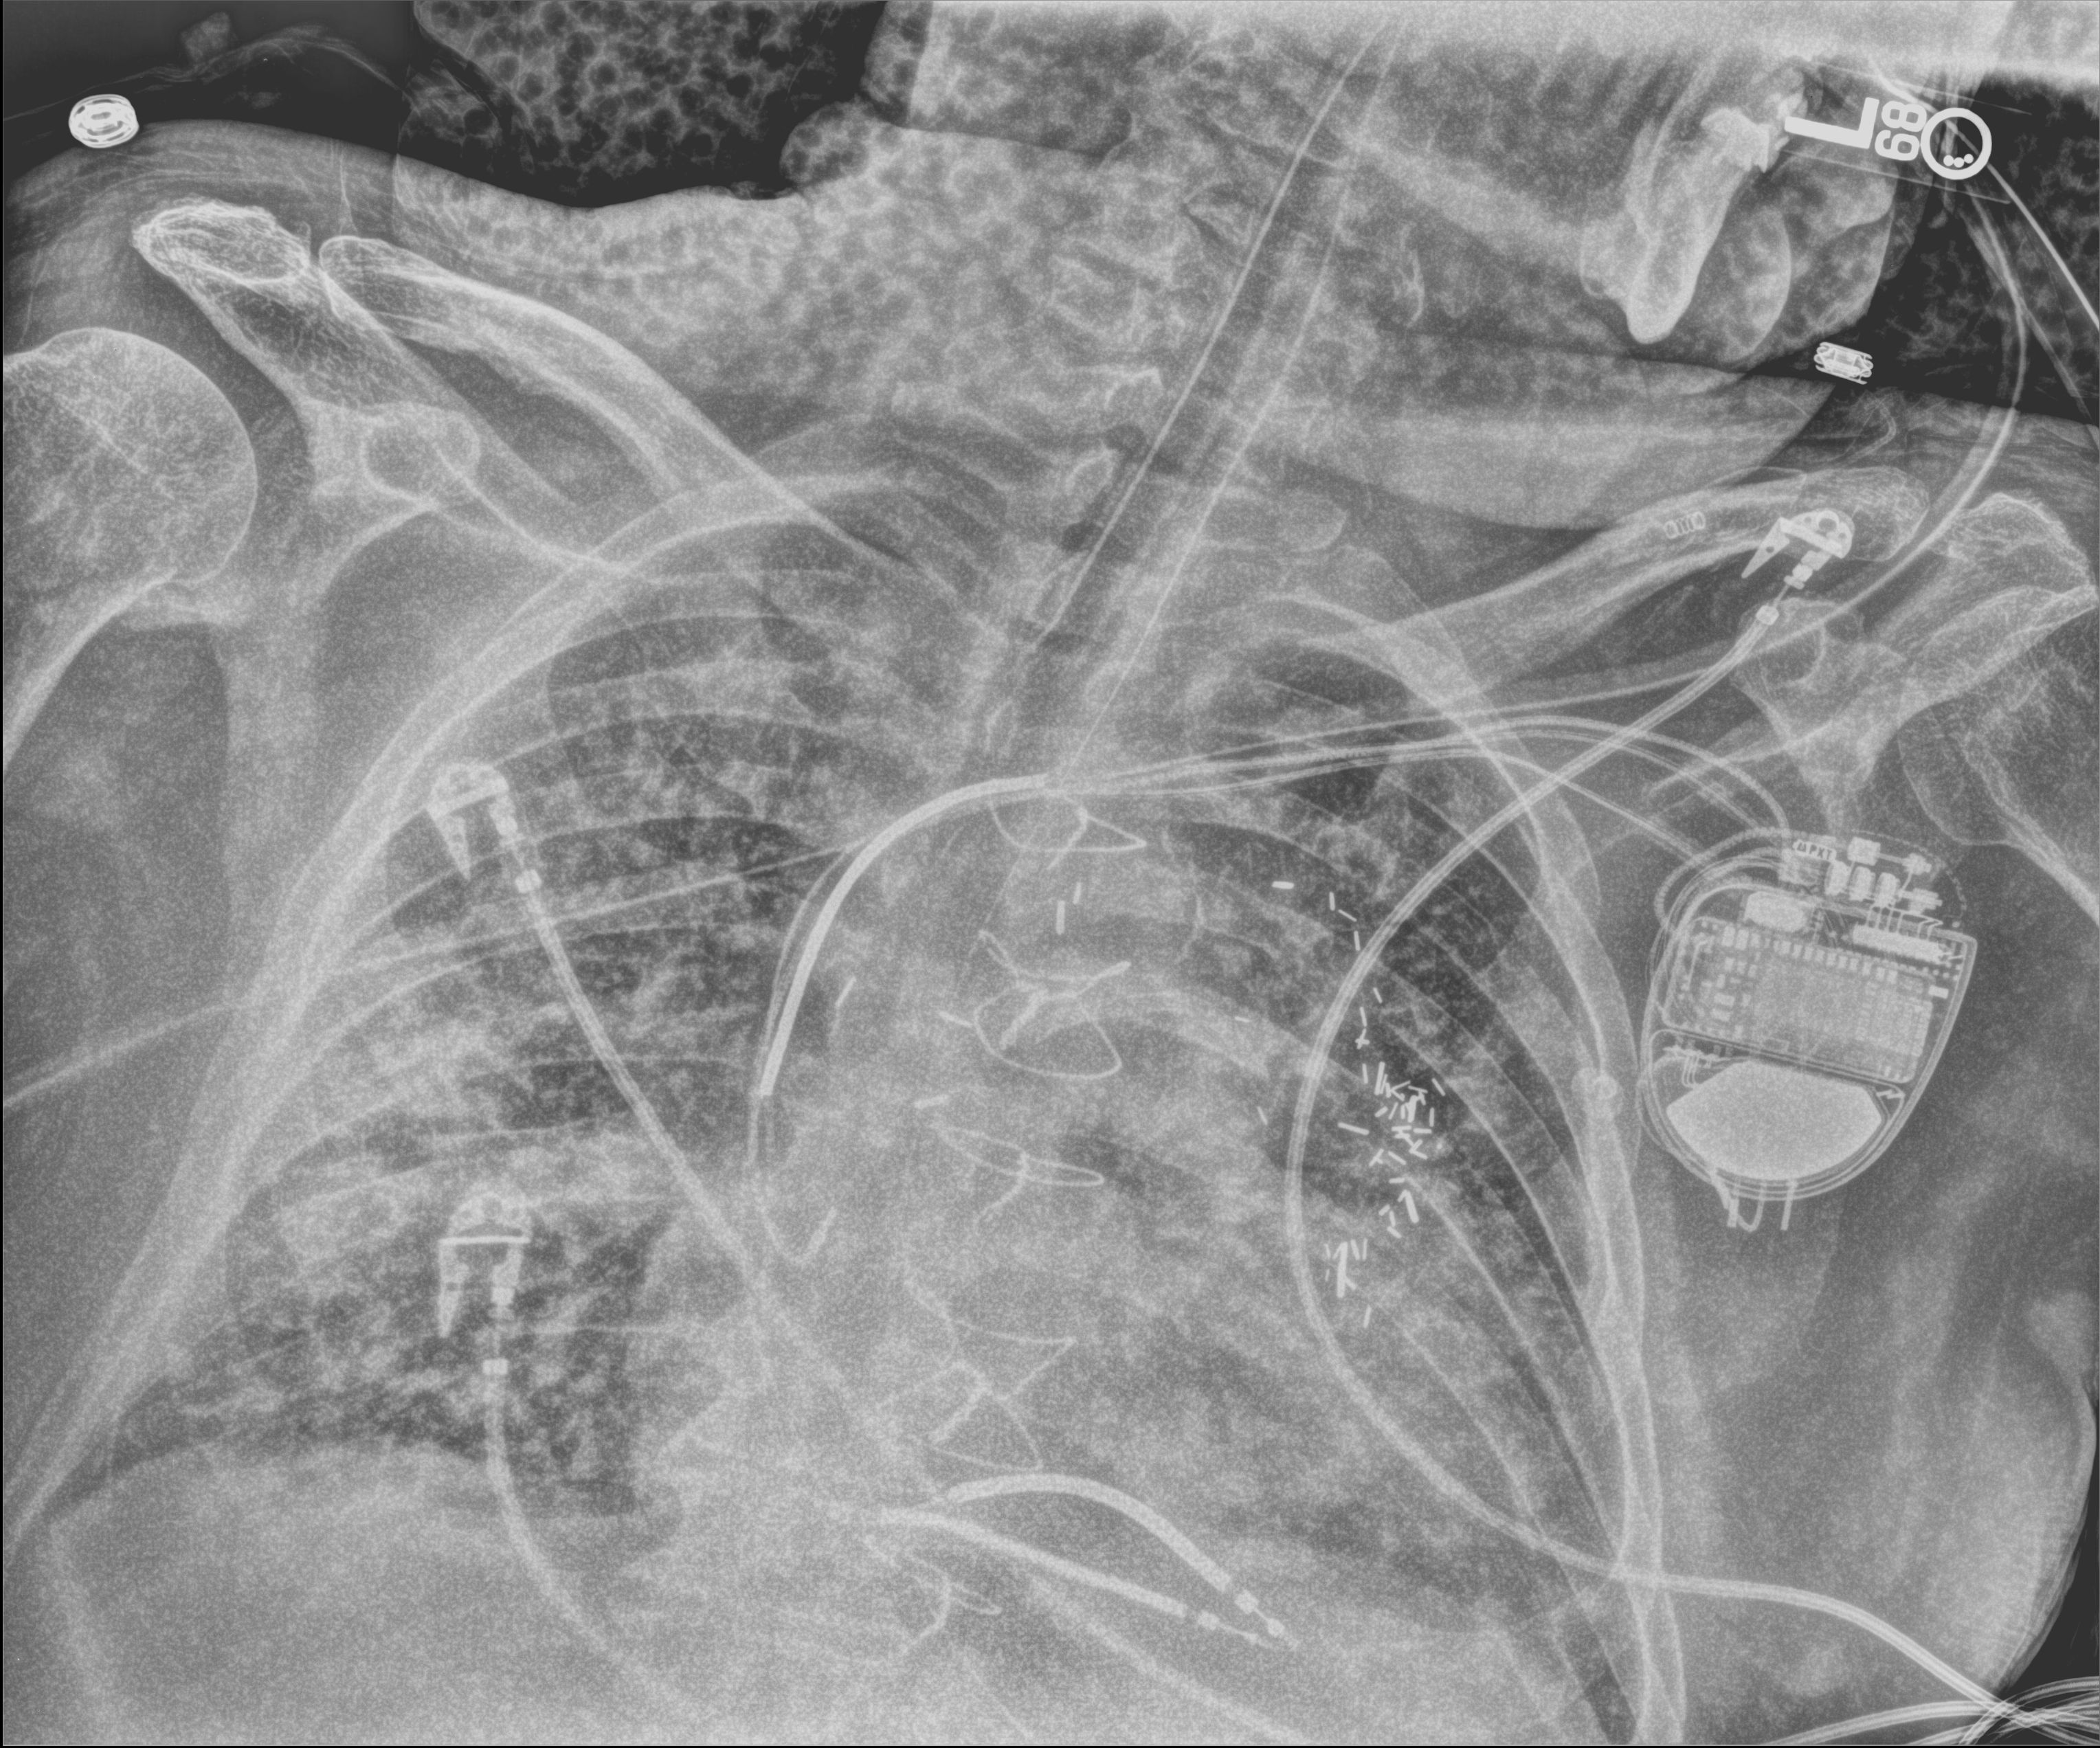
Chest X-ray (portable), anteroposterior (AP) projection. Male patient hospitalised with COVID-19, age 60–74 years.
From the hospital-stay record, not from the radiograph (when in the stay this image was taken is not recorded): other chronic lung disease (admission record): no.